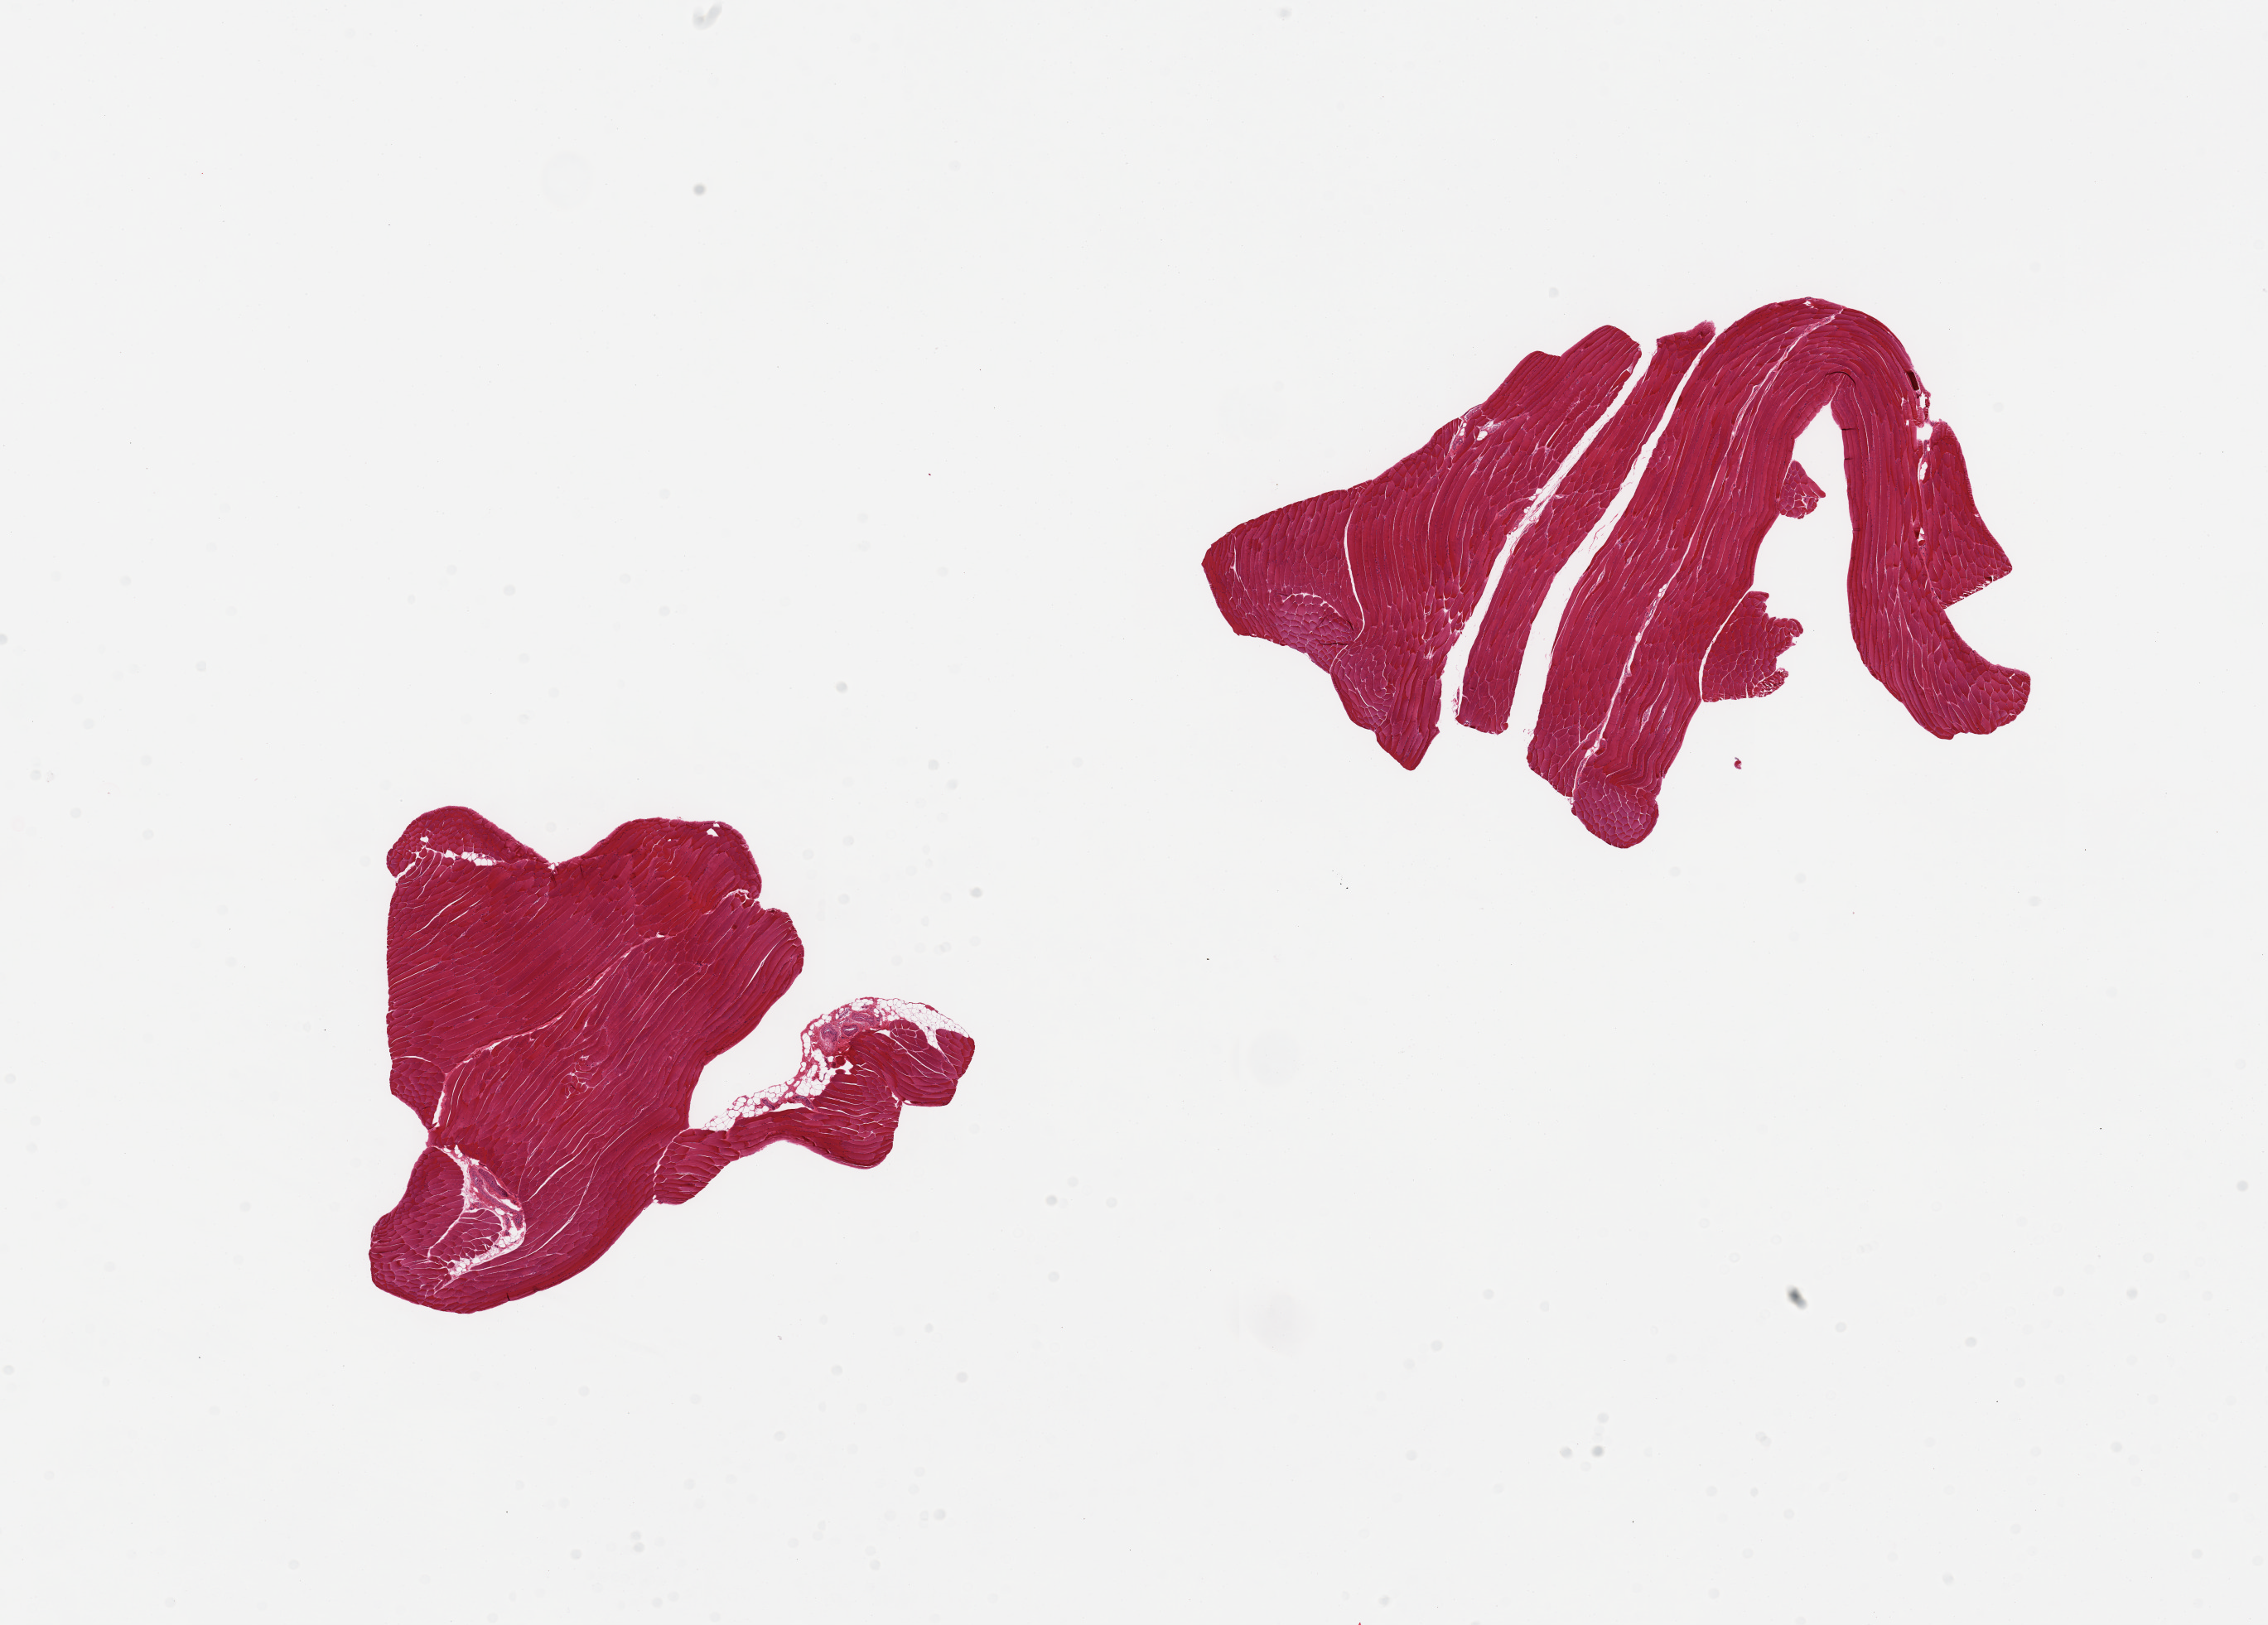
H&E whole-slide image — whole scanned area (about 21.7 x 15.5 mm, acquisition: 20x scan) shown as a low-resolution overview, PAXgene-fixed, paraffin-embedded tissue, target tissue: skeletal muscle, tissue donor sample. Male donor.
* reviewer comment on this tissue sample: 2 pieces, minimal interstitial fat